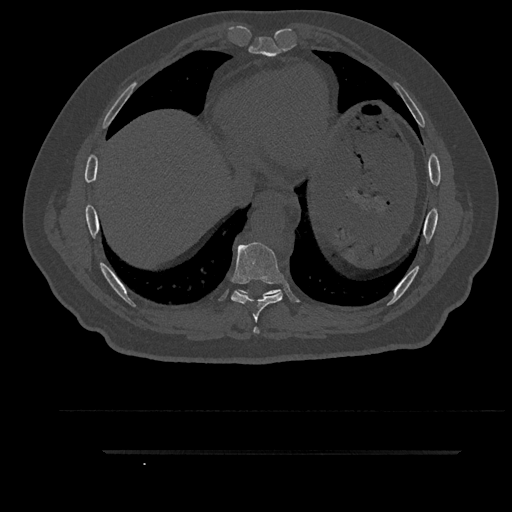
CT including the spine, one axial slice. Position 465 of 797 along the scan axis. Reconstruction kernel Br40s/3. Bone window (W 1800 / L 400 HU). 0.5 mm slice thickness. 512 × 512 image matrix, field of view 432 × 432 mm. Patient: male, 63 years. From the clinical record (not read from this slice): primary cancer: renal; vertebrae with lytic lesions (as recorded): T8.
Annotated regions visible in this slice (semi-automatically segmented with operator editing):
- T7 vertebra: bounding box (x1, y1, x2, y2) in pixels: (254, 327, 259, 334)
- T8 vertebra: (231, 242, 283, 322)
- T9 vertebra: (238, 289, 281, 296)